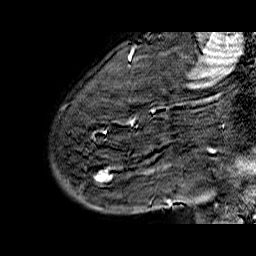
Breast MRI (dynamic contrast-enhanced), one sagittal slice. Dynamic contrast-enhanced series, time point 2 of 6 at this slice position (early post-contrast). 1.5 T. TE 6.5 ms, TR 32.9 ms. 4 mm slice thickness. 256 × 256 image matrix, field of view 200 × 200 mm. Female patient. From the clinical record (not read from this slice): setting: breast cancer imaged before/during neoadjuvant chemotherapy; receptor status: HR-positive, HER2-negative.
Annotated regions visible in this slice (semi-automatically segmented with operator editing):
- analysis volume of interest (the breast-tissue region the enhancement analysis was run in; not a lesion): bounding box [x1, y1, x2, y2] px = [52, 74, 176, 210]
- tumour enhancement mask (voxels above the 100 % enhancement threshold inside the analysis volume of interest): [94, 169, 172, 206]